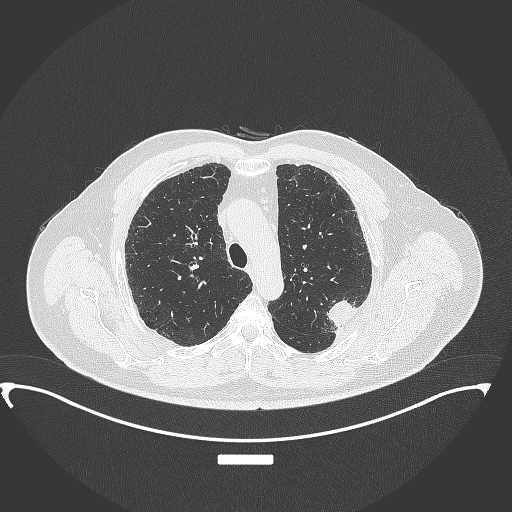
Chest CT, one axial slice; position 267 of 350 along the scan axis; lung window (W 1500 / L -600 HU); 1 mm slice thickness; 512 × 512 image matrix, field of view 459 × 459 mm. Patient: male, 64 years. Case-level facts recorded for this patient, not image findings: clinical TNM (as recorded): T1c N1 M1.
Structures marked on this image (bounding box drawn by a radiologist):
- lung tumour (recorded histology: adenocarcinoma): bounding box [x1, y1, x2, y2] px = [324, 296, 362, 329]